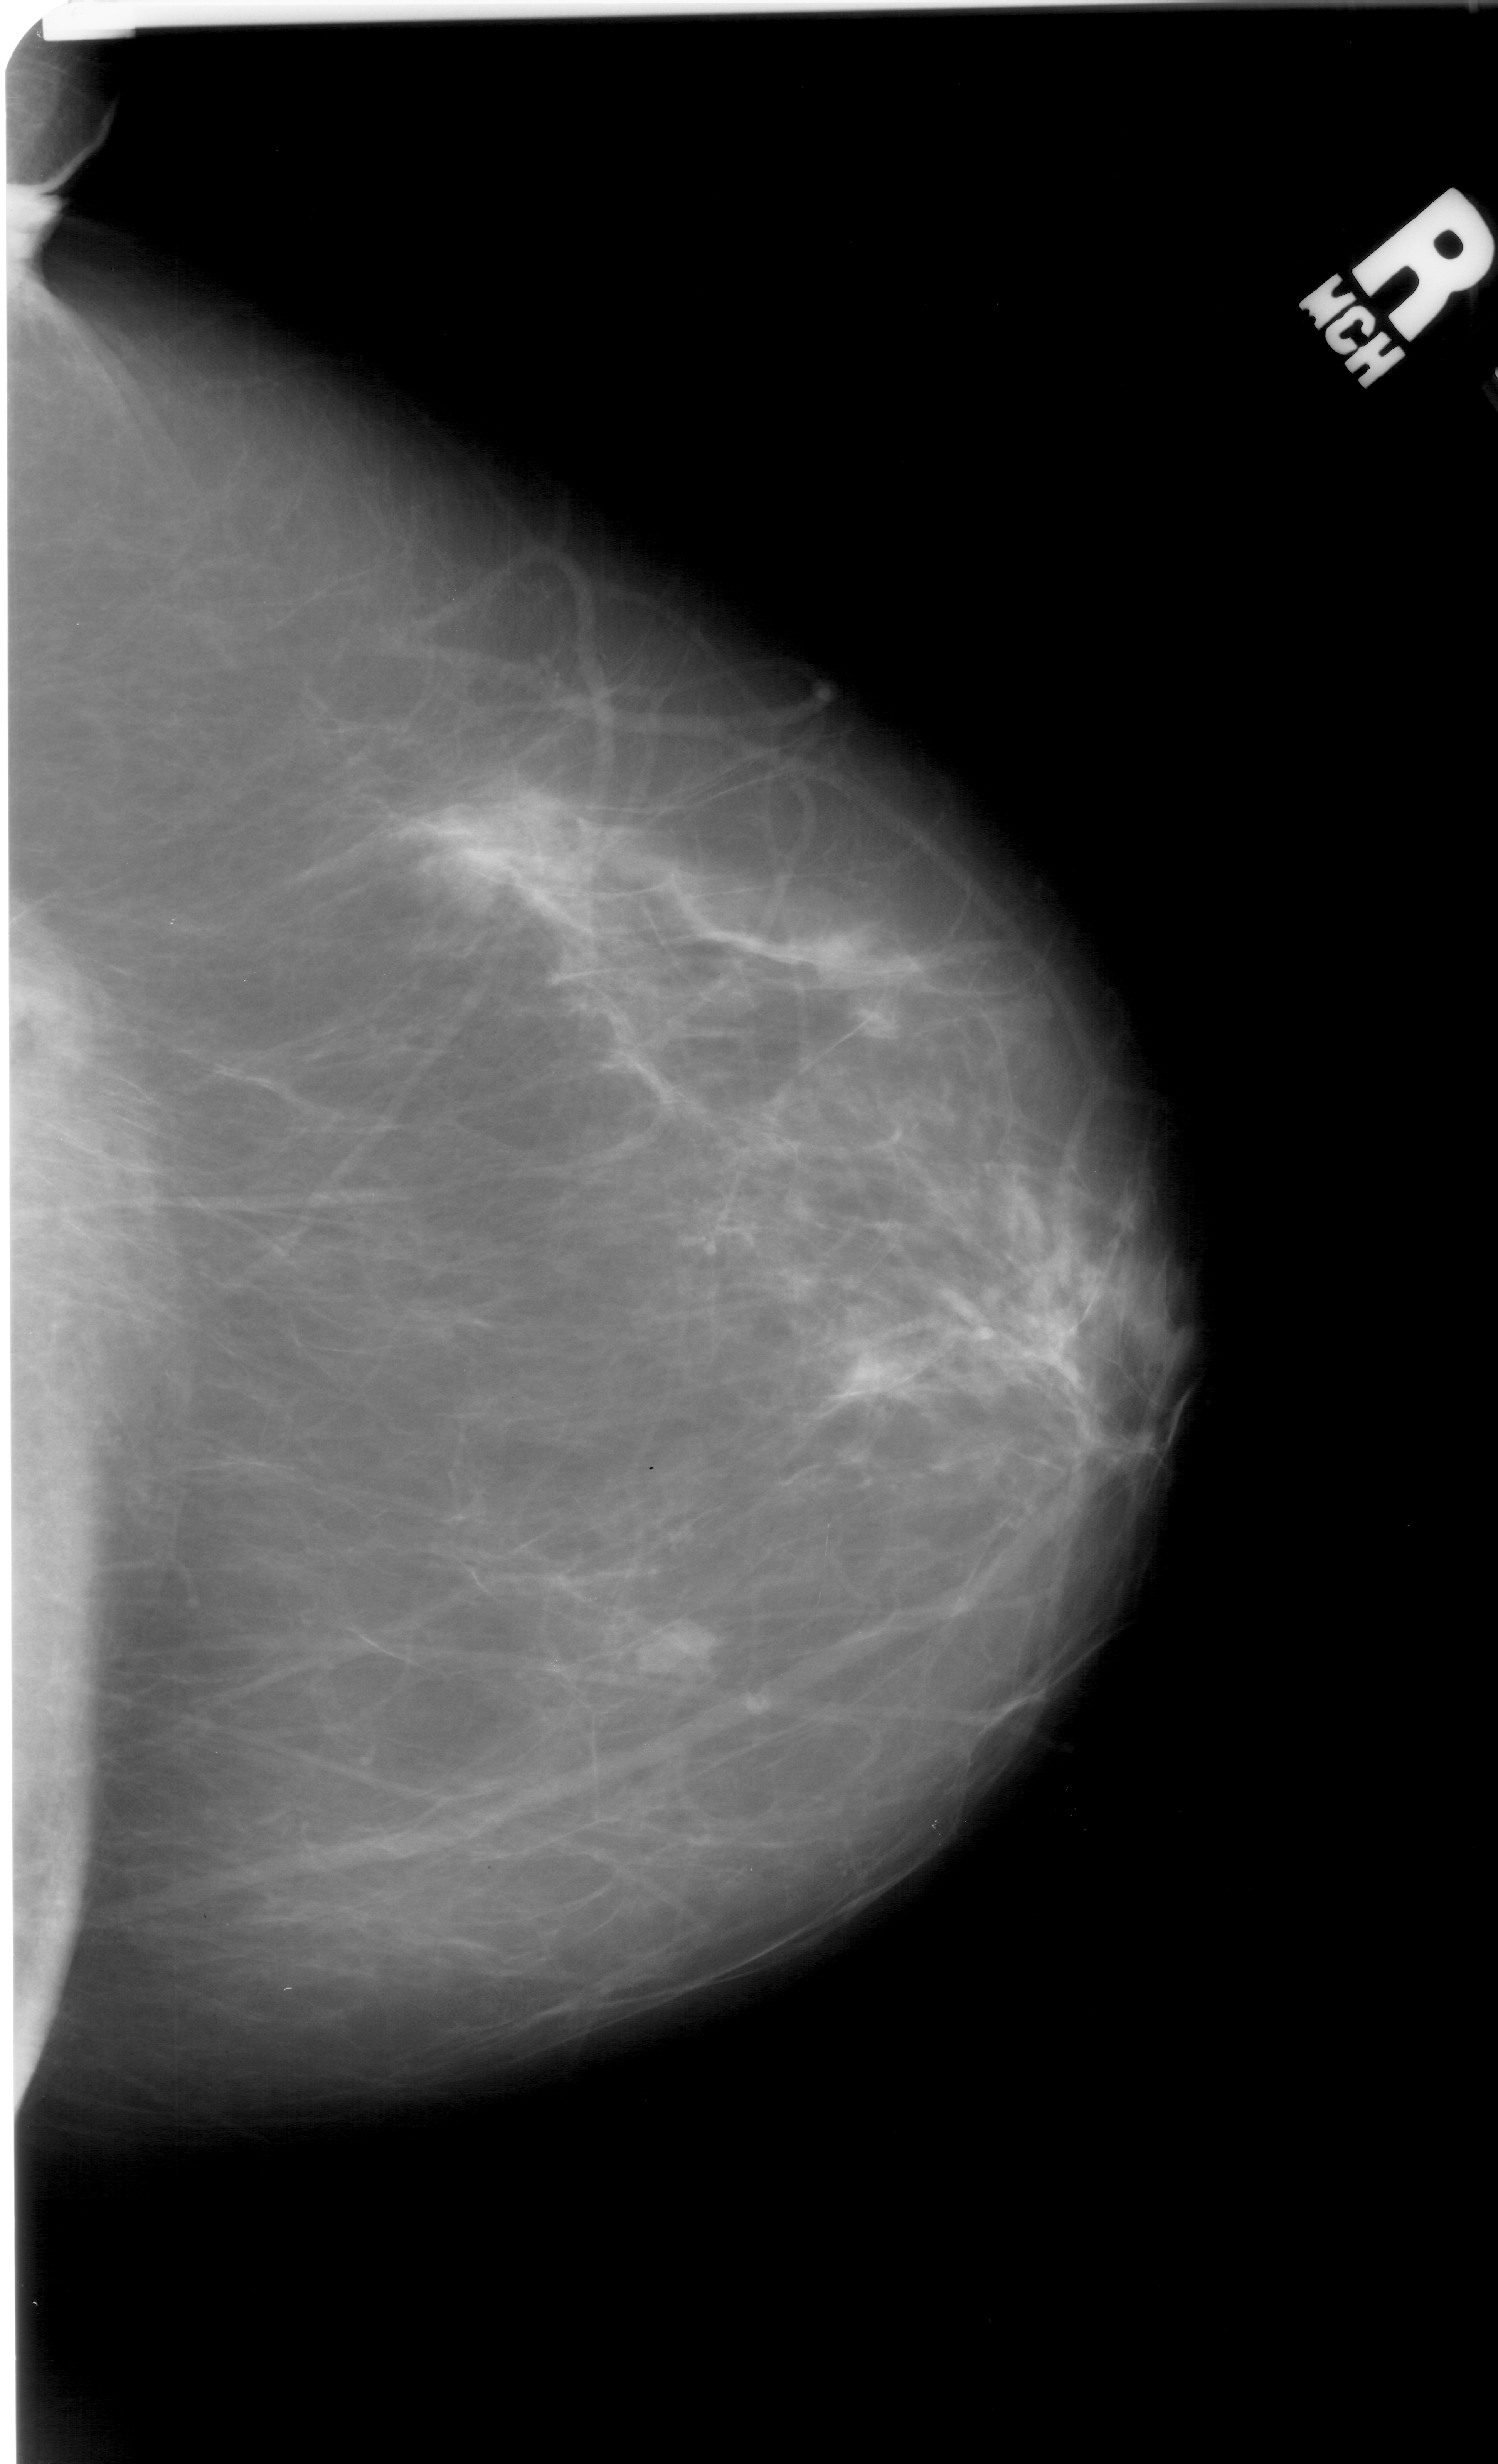
Digitized screen-film mammogram. Right breast. Craniocaudal (CC) view. BI-RADS breast density category 2 (scale 1–4). 1498 × 2464 image matrix.
Expert-marked regions of interest on this film, with their recorded descriptors:
- mass, shape lobulated, margins ill defined; BI-RADS assessment category 4; pathology result (as recorded, not read from the image): malignant: bounding box (x1, y1, x2, y2) in pixels: (639, 1613, 730, 1675)